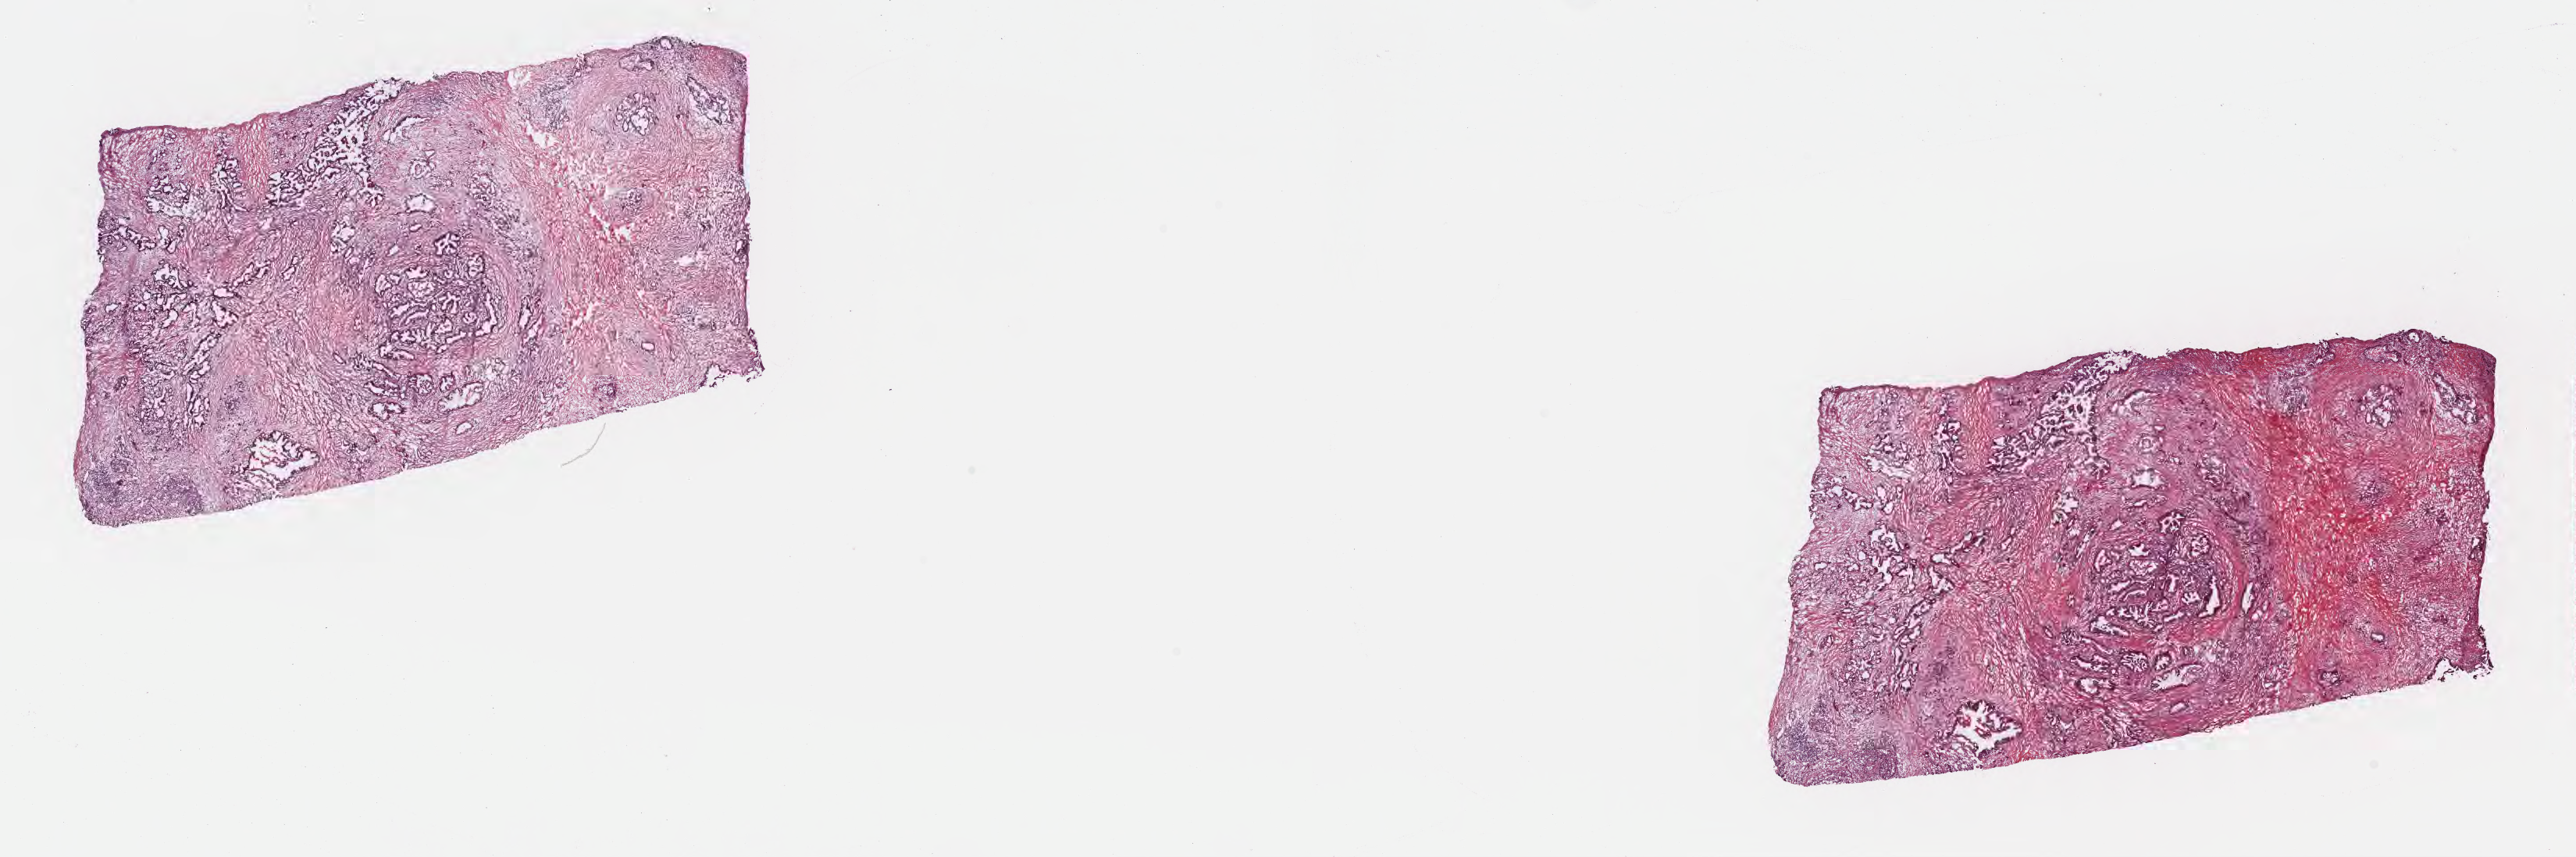
Digitized hematoxylin and eosin (H&E)-stained section, shown as a low-resolution overview of the whole scanned area (about 26.7 x 8.9 mm), frozen section (tissue freezing medium), specimen: primary tumor, site: tail of pancreas. Male, age 74 years at initial diagnosis. Tumor grade: G2 (moderately differentiated). Composition of this section per pathologist review: tumor cells 40%, tumor nuclei 50%, stromal cells 60%, necrosis 0%, normal cells 0%. Inflammatory infiltration, as recorded: lymphocyte infiltration 0%, monocyte infiltration 0%, neutrophil infiltration 0%.
AJCC pathologic stage: Stage IB. Histologic diagnosis: Infiltrating duct carcinoma, NOS.